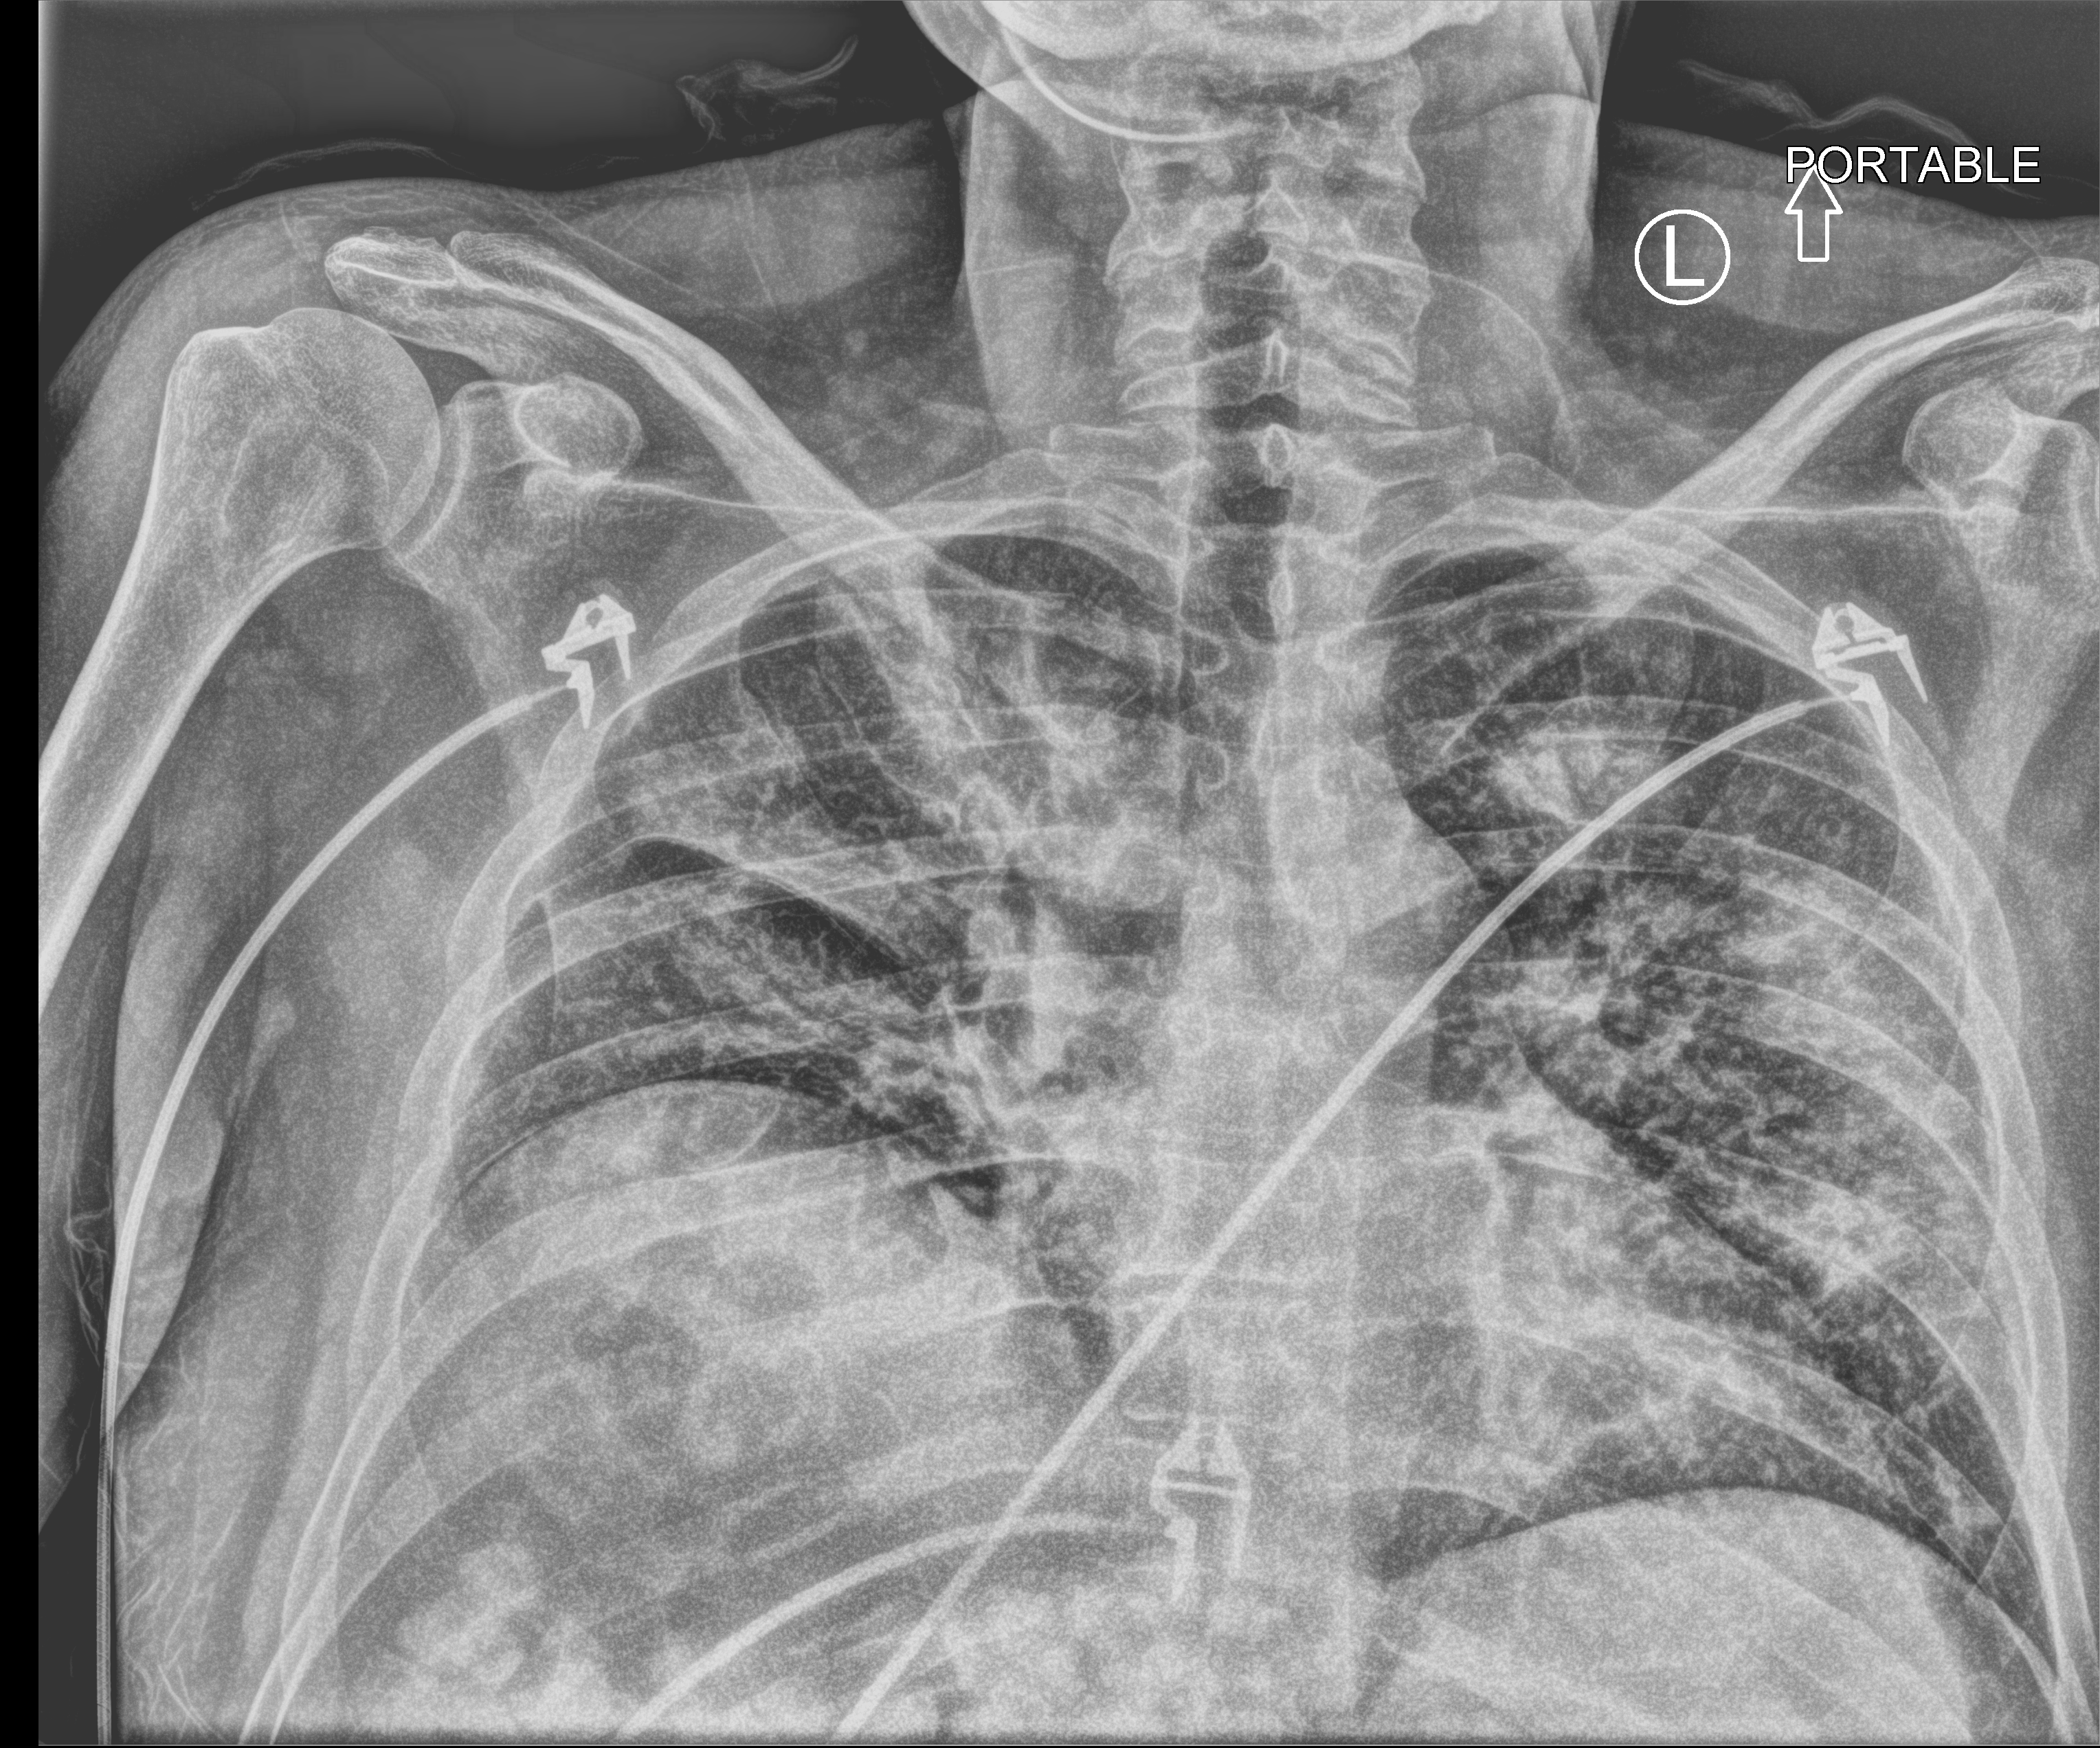
Chest X-ray (portable), anteroposterior (AP) projection. Male patient hospitalised with COVID-19, age 18–59 years.
Hospital-stay facts (about this admission, not read from this image; timing relative to this image not recorded):
- admitted to intensive care during this hospital stay: yes
- COPD (admission record): no